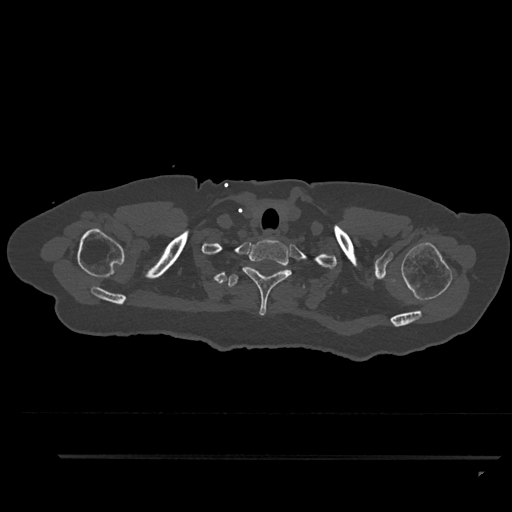
CT including the spine, one axial slice. Bone window (W 1800 / L 400 HU). 0.5 mm slice thickness. 512 × 512 image matrix. Female patient, age 44 years. From the clinical record (not read from this slice): primary cancer: renal; vertebrae with lytic lesions (as recorded): L1.
Structures marked on this image (semi-automatic segmentation, software-assisted and operator-edited):
- T1 vertebra: box from (x=242, y=237) to (x=292, y=316) px
- T2 vertebra: (x=228, y=274)–(x=305, y=288)